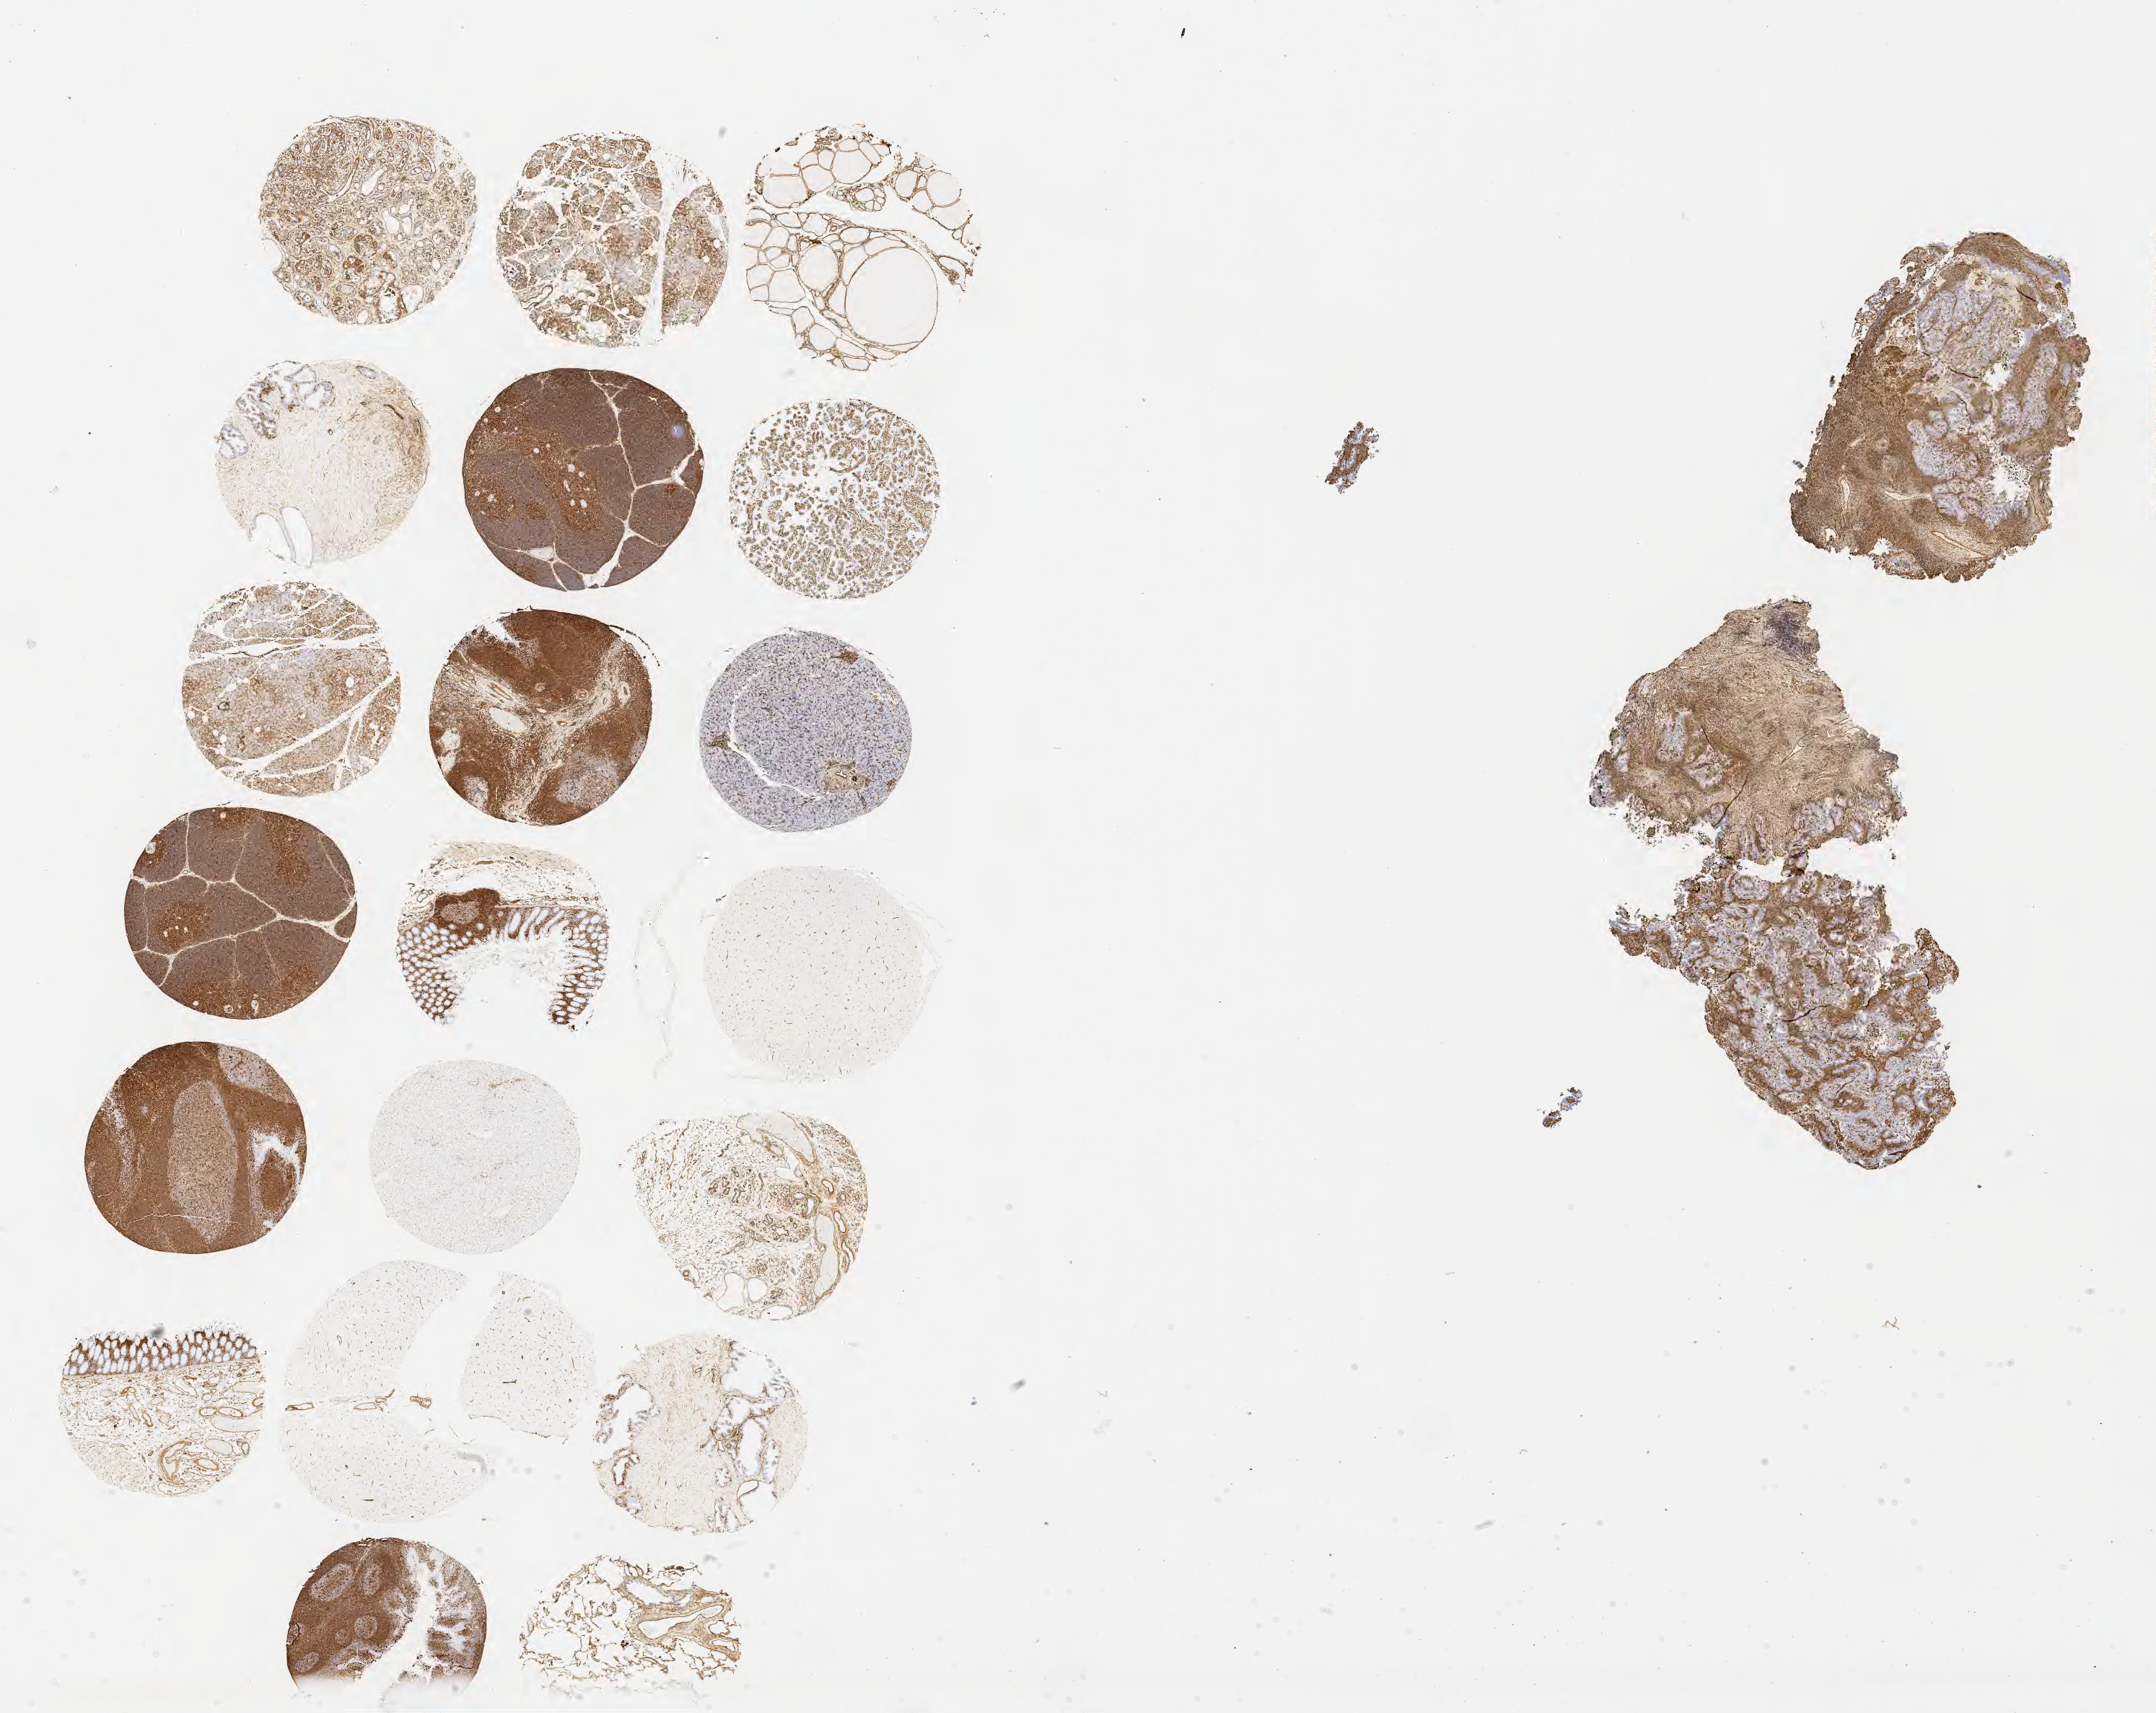
Immunohistochemistry (IHC) whole-slide image stained for vimentin — whole scanned area (about 24.1 x 19.2 mm) shown as a low-resolution overview, tumor tissue, site: cervix. Patient female; 48 years old.
Histologic diagnosis: Adenocarcinoma, NOS.